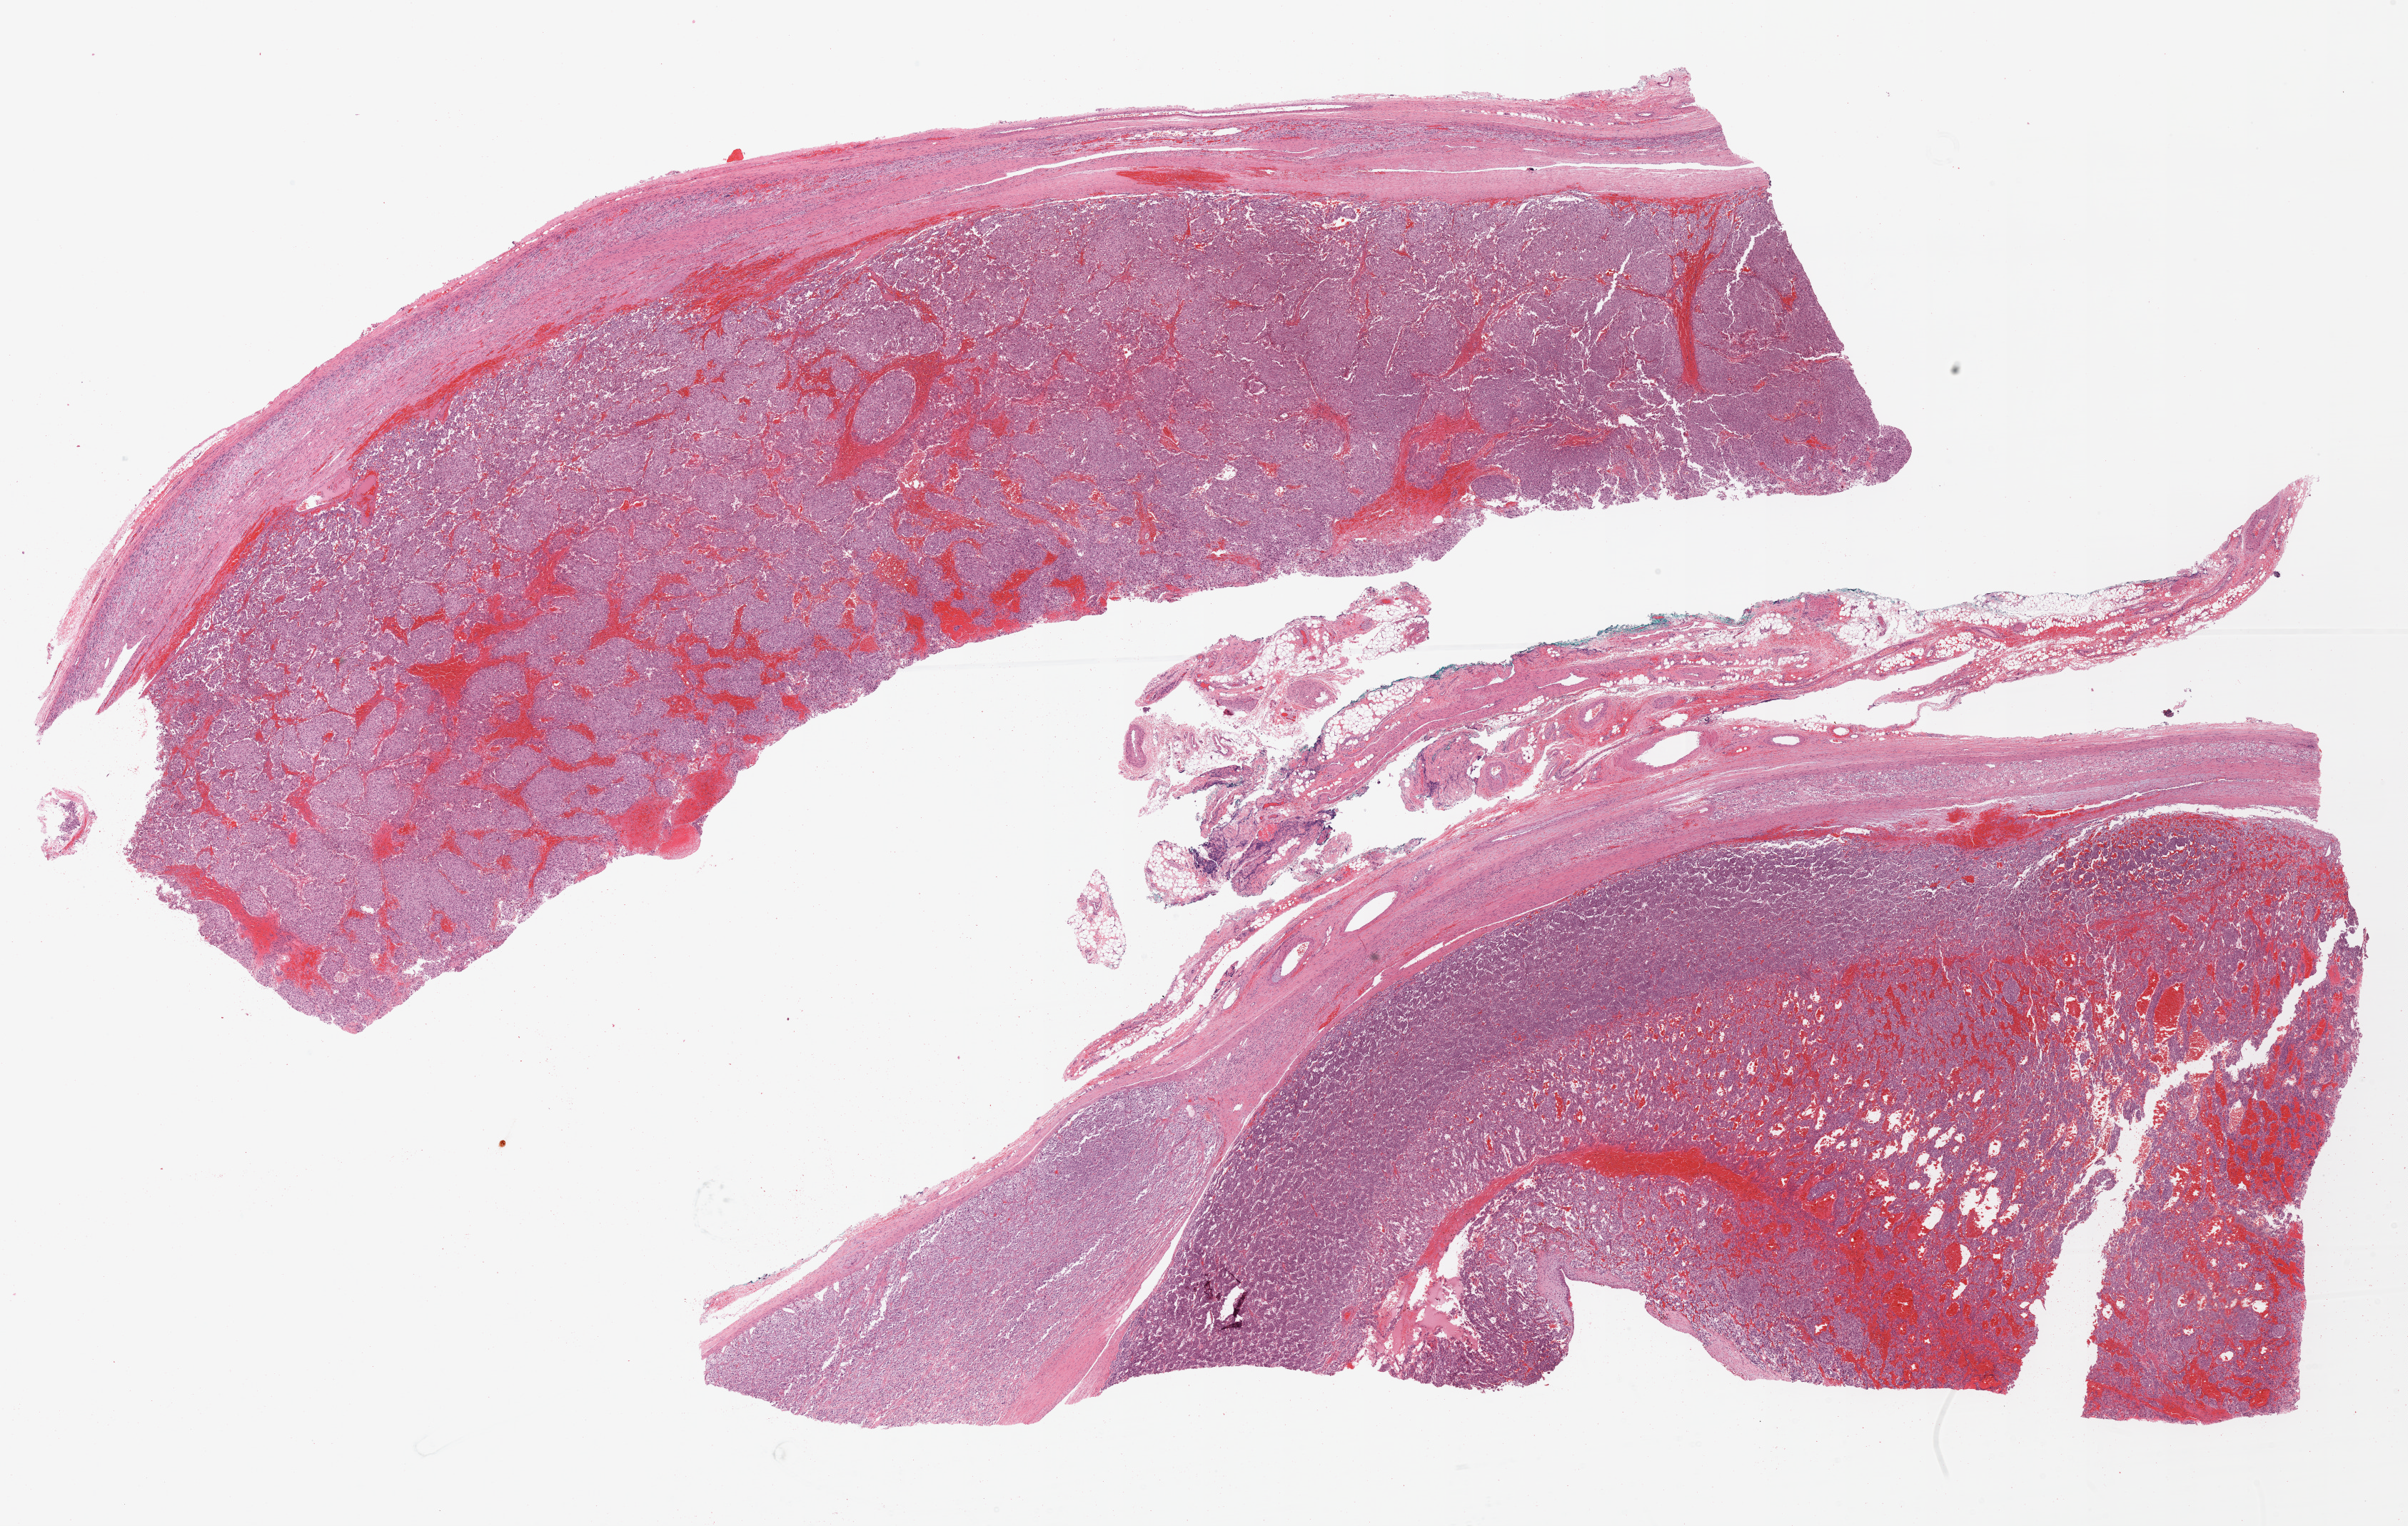
Whole-slide histology image, Hematoxylin and eosin (H&E) stained, a low-resolution overview of the entire scanned area, about 26.9 x 17.1 mm (acquisition: 20x scan); formalin-fixed paraffin-embedded (FFPE) diagnostic section; adrenal gland, primary tumour sample. Patient: female, age at initial diagnosis 21 years.
- diagnosis: Pheochromocytoma, malignant
- laterality: left